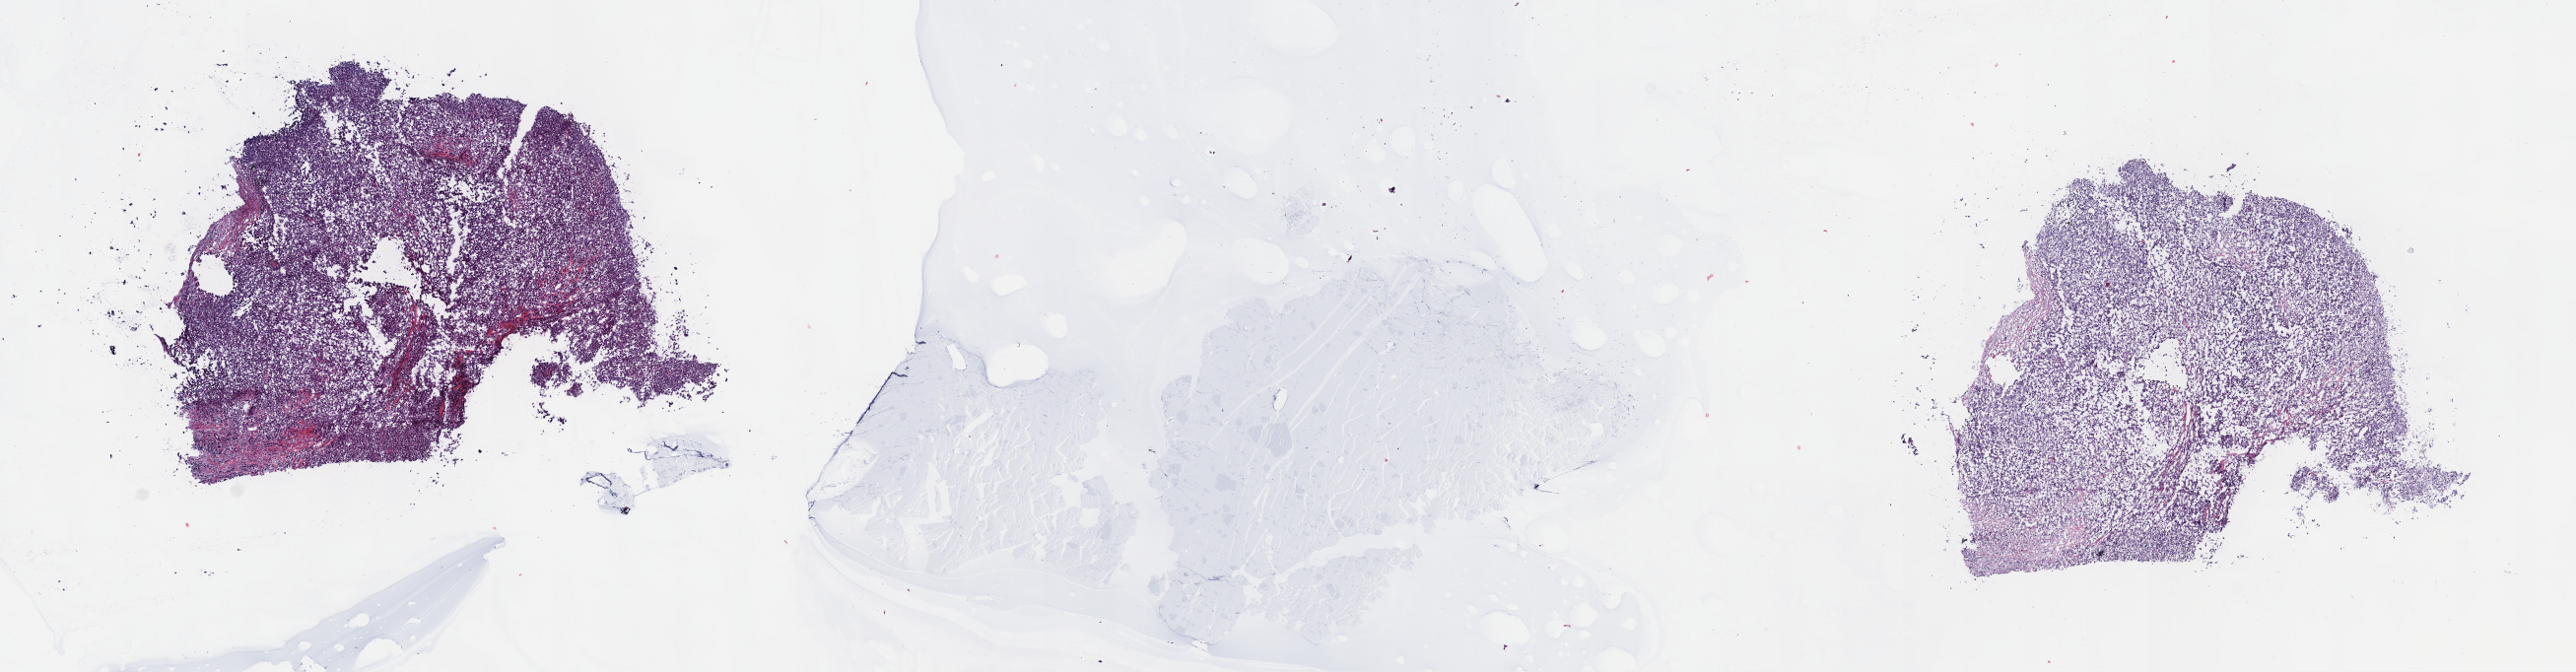
H&E whole-slide image, a low-resolution overview of the entire scanned area, about 21.1 x 5.5 mm (slide scanned at 40x). Frozen section from the top of the tissue portion. Metastatic tumour sample, sampled site not recorded. Male, age 65 years at initial diagnosis. Composition of this section per pathologist review: tumour cells 100%, tumour nuclei 75%, normal cells 0%, stromal cells 0%, necrosis 0%. Infiltration values recorded for this section: lymphocyte infiltration 2%, monocyte infiltration 0%, neutrophil infiltration 0%.
* this section: metastatic tumour tissue
* patient diagnosis: Lentigo maligna melanoma